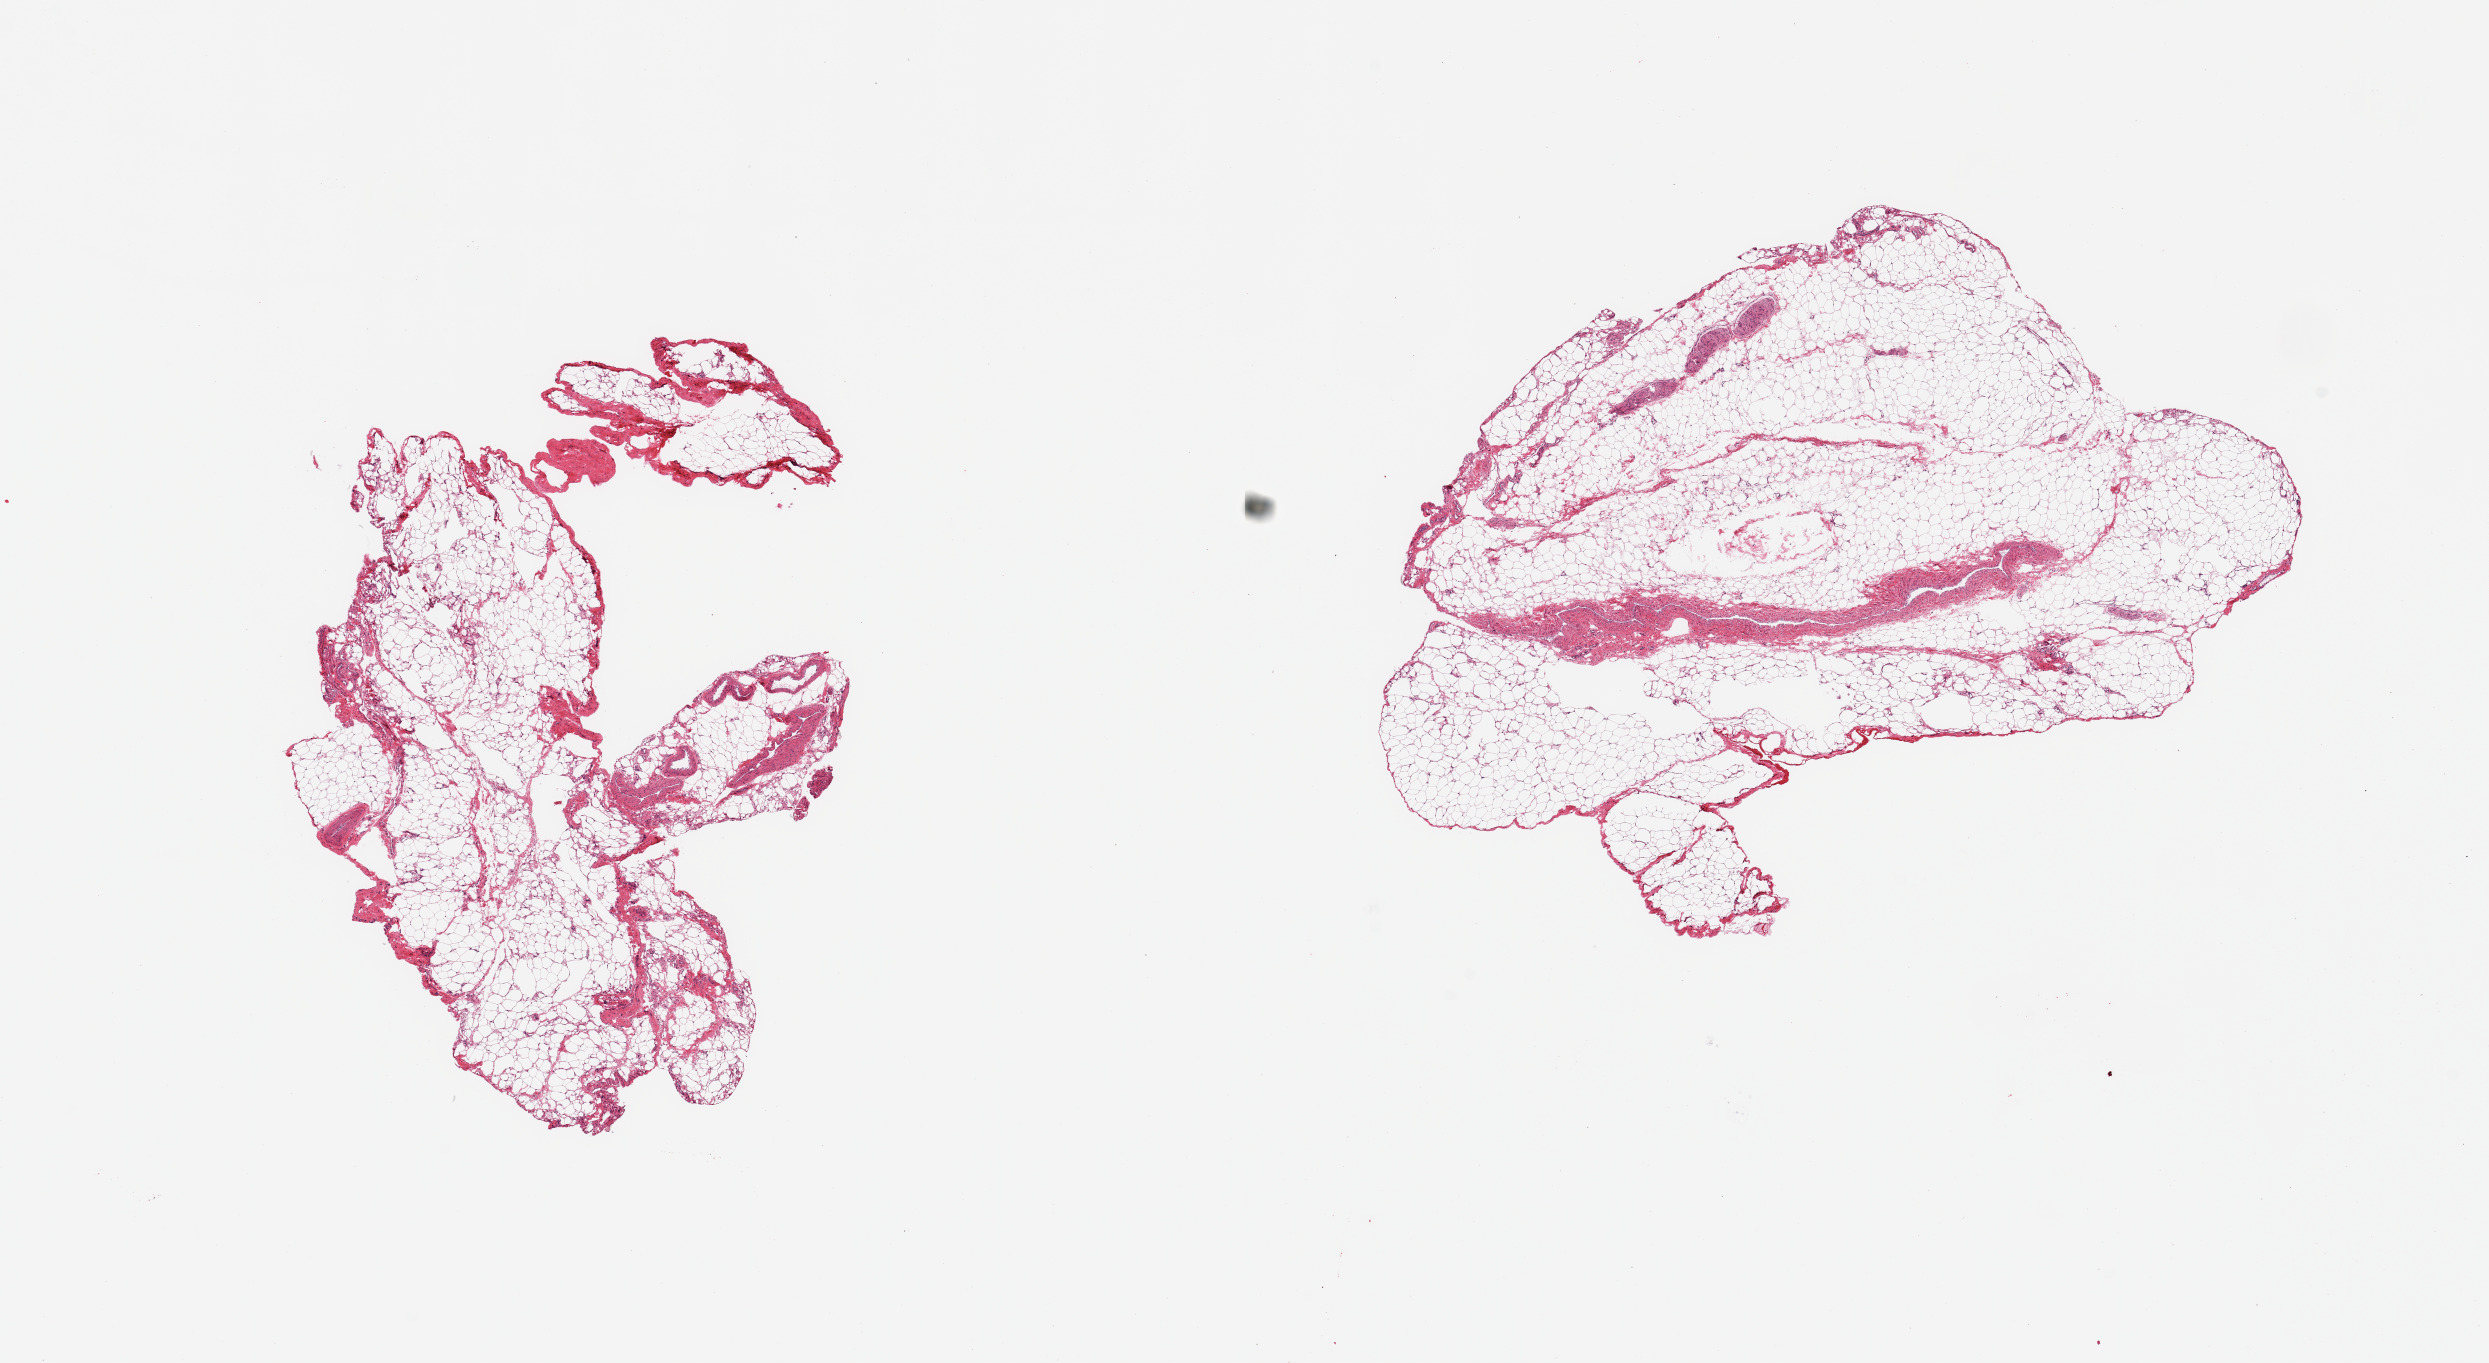
Digitized H&E-stained section — whole scanned area (about 19.7 x 10.8 mm, from a 20x scan) shown as a low-resolution overview. PAXgene-fixed paraffin-embedded (PFPE) section. Target tissue: omentum. Tissue donor sample. Male donor.
Pathologist's review note for this sample: 2 pieces, ~20% fascia/vascular elements.